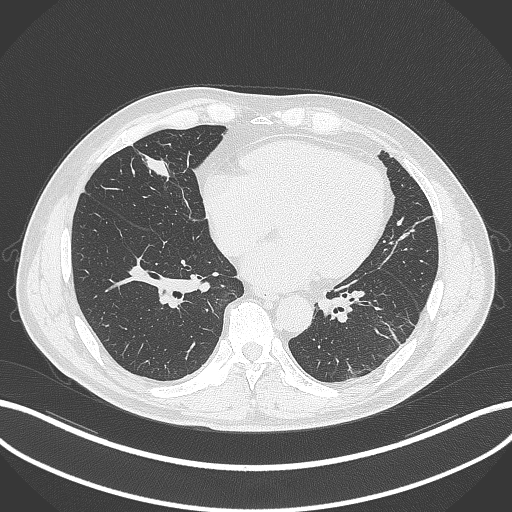
Chest CT, one axial slice; position 99 of 399 along the scan axis; 120 kVp; lung window (W 1500 / L -600 HU); 1 mm slice thickness; 512 × 512 image matrix, field of view 400 × 400 mm. Patient: male, 59 years. From the clinical record (not read from this slice): clinical TNM (as recorded): T2a N1 M0.
Structures marked on this image (rectangle marked by the reading radiologist):
- lung tumour (recorded histology: adenocarcinoma): bounding box [x1, y1, x2, y2] px = [138, 147, 176, 189]